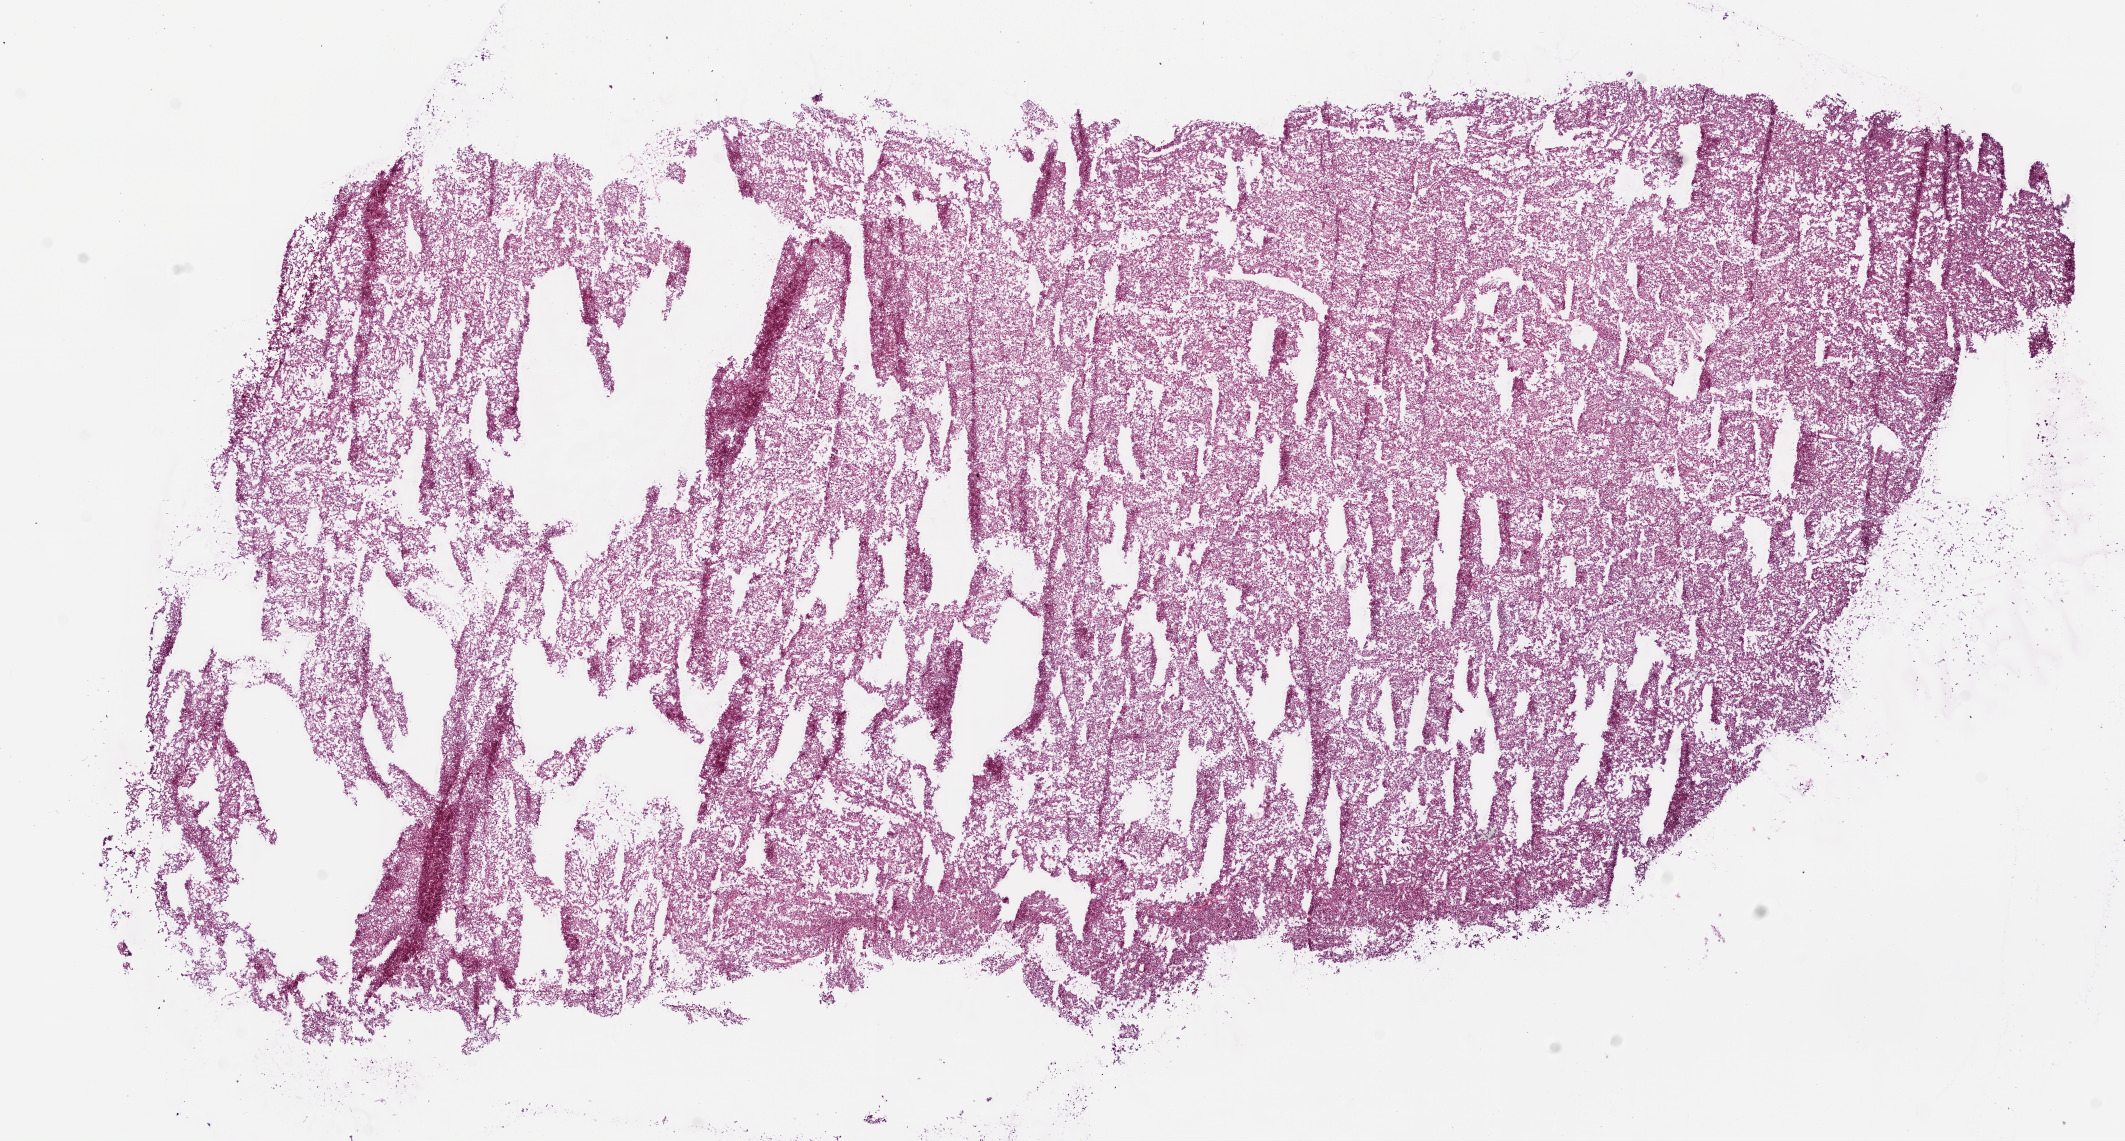
Digitized Hematoxylin and eosin (H&E) stained tissue section (whole slide) — a low-resolution overview of the entire scanned area, about 17.1 x 9.2 mm (acquisition: 20x scan); frozen section from the bottom of the tissue portion; sample: primary tumour, kidney. Patient: female, age at initial diagnosis 65 years. Slide review estimates, as recorded: tumour cells 95%, tumour nuclei 85%.
Histologic diagnosis: Clear cell adenocarcinoma, NOS.